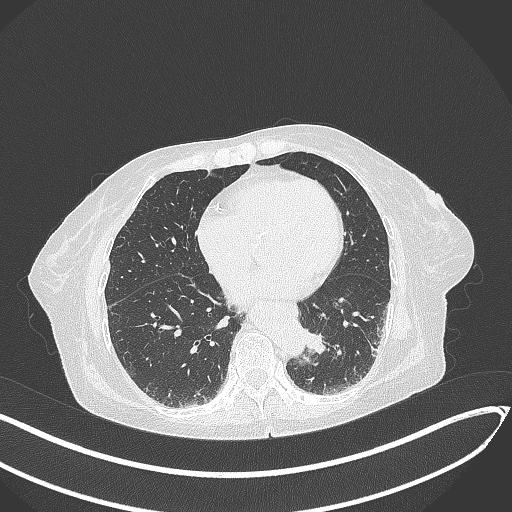
Chest CT, one axial slice. Slice 78 of 324 in the series (ordered by position). Reconstruction kernel B70f. Lung window (W 1500 / L -600 HU). 512 × 512 image matrix. Female patient, age 82 years. Case-level facts recorded for this patient, not image findings: clinical TNM (as recorded): T1b N0 M1.
Outlined on this slice (rectangle marked by the reading radiologist):
- lung tumour (recorded histology: adenocarcinoma): box from (x=300, y=322) to (x=330, y=354) px